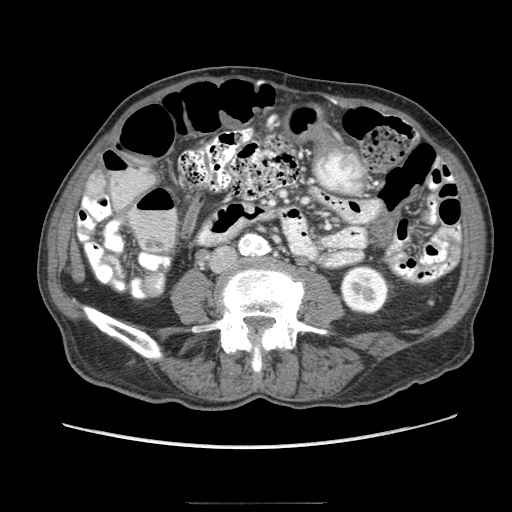
Contrast-enhanced abdominal CT (liver protocol), one axial slice. Position 7 of 83 along the scan axis. 140 kVp. Soft-tissue window (W 400 / L 40 HU). 2.5 mm slice thickness. 512 × 512 image matrix. Case-level facts recorded for this patient, not image findings: diagnosis: hepatocellular carcinoma (patient treated with transarterial chemoembolisation; whether this scan precedes or follows treatment is not stated here); TNM stage (as recorded): Stage-I.
Structures marked on this image (semi-automatic segmentation, software-assisted and operator-edited):
- liver parenchyma outside the tumour (the mass and vessels are separate outlines, so this box may not span the whole liver): box from (x=82, y=170) to (x=106, y=203) px
- liver vessels: (x=82, y=197)–(x=90, y=205)